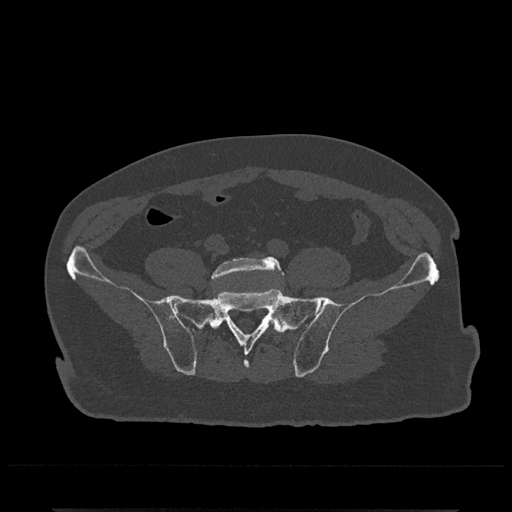
CT including the spine, one axial slice; position 42 of 797 along the scan axis; 120 kVp; bone window (W 1800 / L 400 HU); 512 × 512 image matrix, field of view 393 × 393 mm. Male patient, age 67 years. Case-level facts recorded for this patient, not image findings: primary cancer: prostate.
Annotated regions visible in this slice (semi-automatically segmented with operator editing):
- L5 vertebra: box from (x=211, y=257) to (x=284, y=328) px